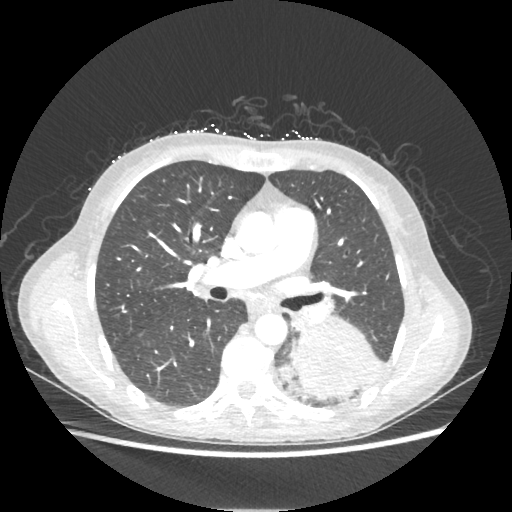
Chest CT, one axial slice; position 124 of 221 along the scan axis; lung window (W 1500 / L -600 HU); 1.25 mm slice thickness; 512 × 512 image matrix, field of view 360 × 360 mm. Female patient, age 53 years. Case-level facts recorded for this patient, not image findings: clinical TNM (as recorded): T3 N0 M0.
Annotated regions visible in this slice (rectangle marked by the reading radiologist):
- lung tumour (recorded histology: adenocarcinoma): box from (x=292, y=314) to (x=377, y=400) px